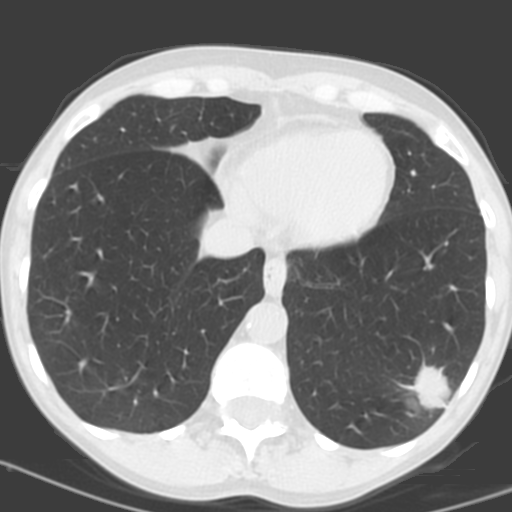
Low-dose screening chest CT, axial slice, baseline annual screen, lung window (W 1500 / L -600 HU), 3.2 mm slice thickness, standard (soft-tissue) reconstruction kernel (C), 120 kVp. Female participant, aged 56 years at enrolment. Current smoker at enrolment.
Lesion marked by an expert reader, bounding box <393,356,468,424> (left, top, right, bottom; pixels). Reader record for this screening exam (exam-level; its link to the box is not recorded): non-calcified nodule or mass ≥4 mm, left lower lobe, 31 × 23 mm, poorly defined margins, soft tissue attenuation, pre-existing on the prior screen: no. Official screen result: positive, change unspecified: nodule(s) >= 4 mm or enlarging nodule(s), mass(es), or other non-specific abnormalities suspicious for lung cancer. Later outcome: lung cancer diagnosed 27 days after this screen — squamous cell carcinoma, NOS, left lower lobe, poorly differentiated (G3), stage IB (AJCC 6th edition), 35 mm at pathology.